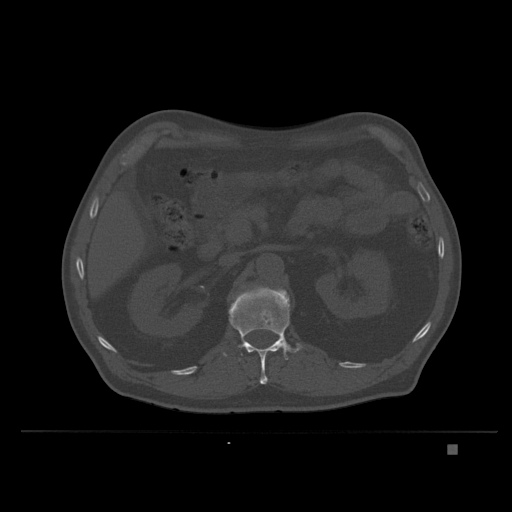
CT including the spine, one axial slice; position 136 of 435 along the scan axis; bone window (W 1800 / L 400 HU); 512 × 512 image matrix, field of view 434 × 434 mm. Male patient, age 73 years. From the clinical record (not read from this slice): primary cancer: skin.
Annotated regions visible in this slice (semi-automatic segmentation, software-assisted and operator-edited):
- L1 vertebra: bounding box (x1, y1, x2, y2) in pixels: (223, 286, 303, 384)